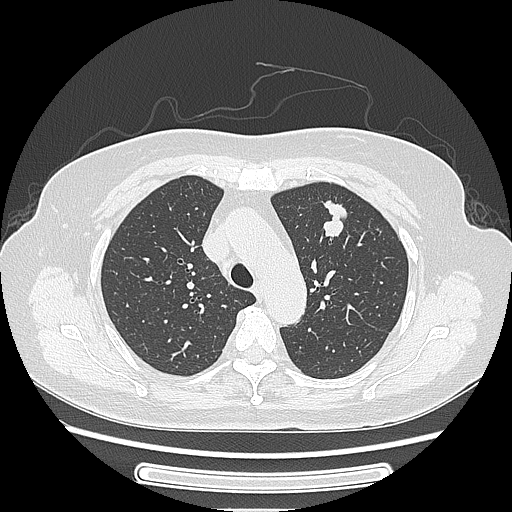
Chest CT, one axial slice. Position 175 of 227 along the scan axis. Reconstruction kernel LUNG. 120 kVp. Lung window (W 1500 / L -600 HU). 512 × 512 image matrix, field of view 363 × 363 mm. Patient: female, 77 years. Case-level facts recorded for this patient, not image findings: clinical TNM (as recorded): T1c N3 M0.
Annotated regions visible in this slice (rectangle marked by the reading radiologist):
- lung tumour (recorded histology: adenocarcinoma): box from (x=313, y=194) to (x=358, y=249) px